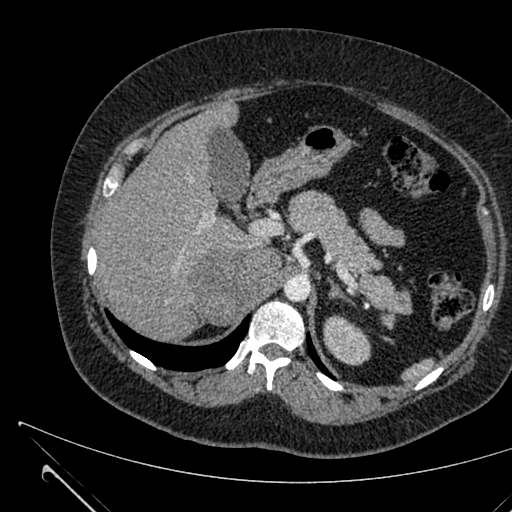
Contrast-enhanced abdominal CT, one axial slice. Slice 451 of 731 in the series (ordered by position). Intravenous contrast given. Soft-tissue window (W 400 / L 40 HU). 1 mm slice thickness. 512 × 512 image matrix, field of view 376 × 376 mm. Patient: female, 36 years. From the clinical record (not read from this slice): diagnosis: adrenocortical carcinoma; tumour side: right adrenal; tumour size at pathology: 10 cm; Ki-67 index: 20 %; stage (as recorded): 4.
Annotated regions visible in this slice (semi-automatically segmented with operator editing):
- mass: bounding box <190,250,280,323> (left, top, right, bottom; pixels)